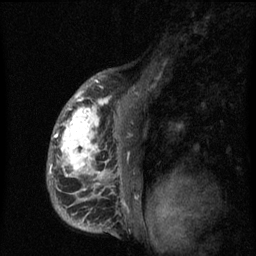
Breast MRI (dynamic contrast-enhanced), one sagittal slice; slice 45 of 60 in the series (ordered by position); dynamic contrast-enhanced series, image 2 of 3 at this slice position (ordered by acquisition); 1.5 T; TE 4.2 ms, TR 8 ms; 2 mm slice thickness; 256 × 256 image matrix. Female patient, age 50 years.
Outlined on this slice (semi-automatic segmentation, software-assisted and operator-edited):
- analysis volume of interest (the breast-tissue region the enhancement analysis was run in; not a lesion): bounding box (x1, y1, x2, y2) in pixels: (47, 90, 142, 216)
- tumour enhancement mask (voxels above the 70 % enhancement threshold inside the analysis volume of interest): (49, 90, 125, 206)